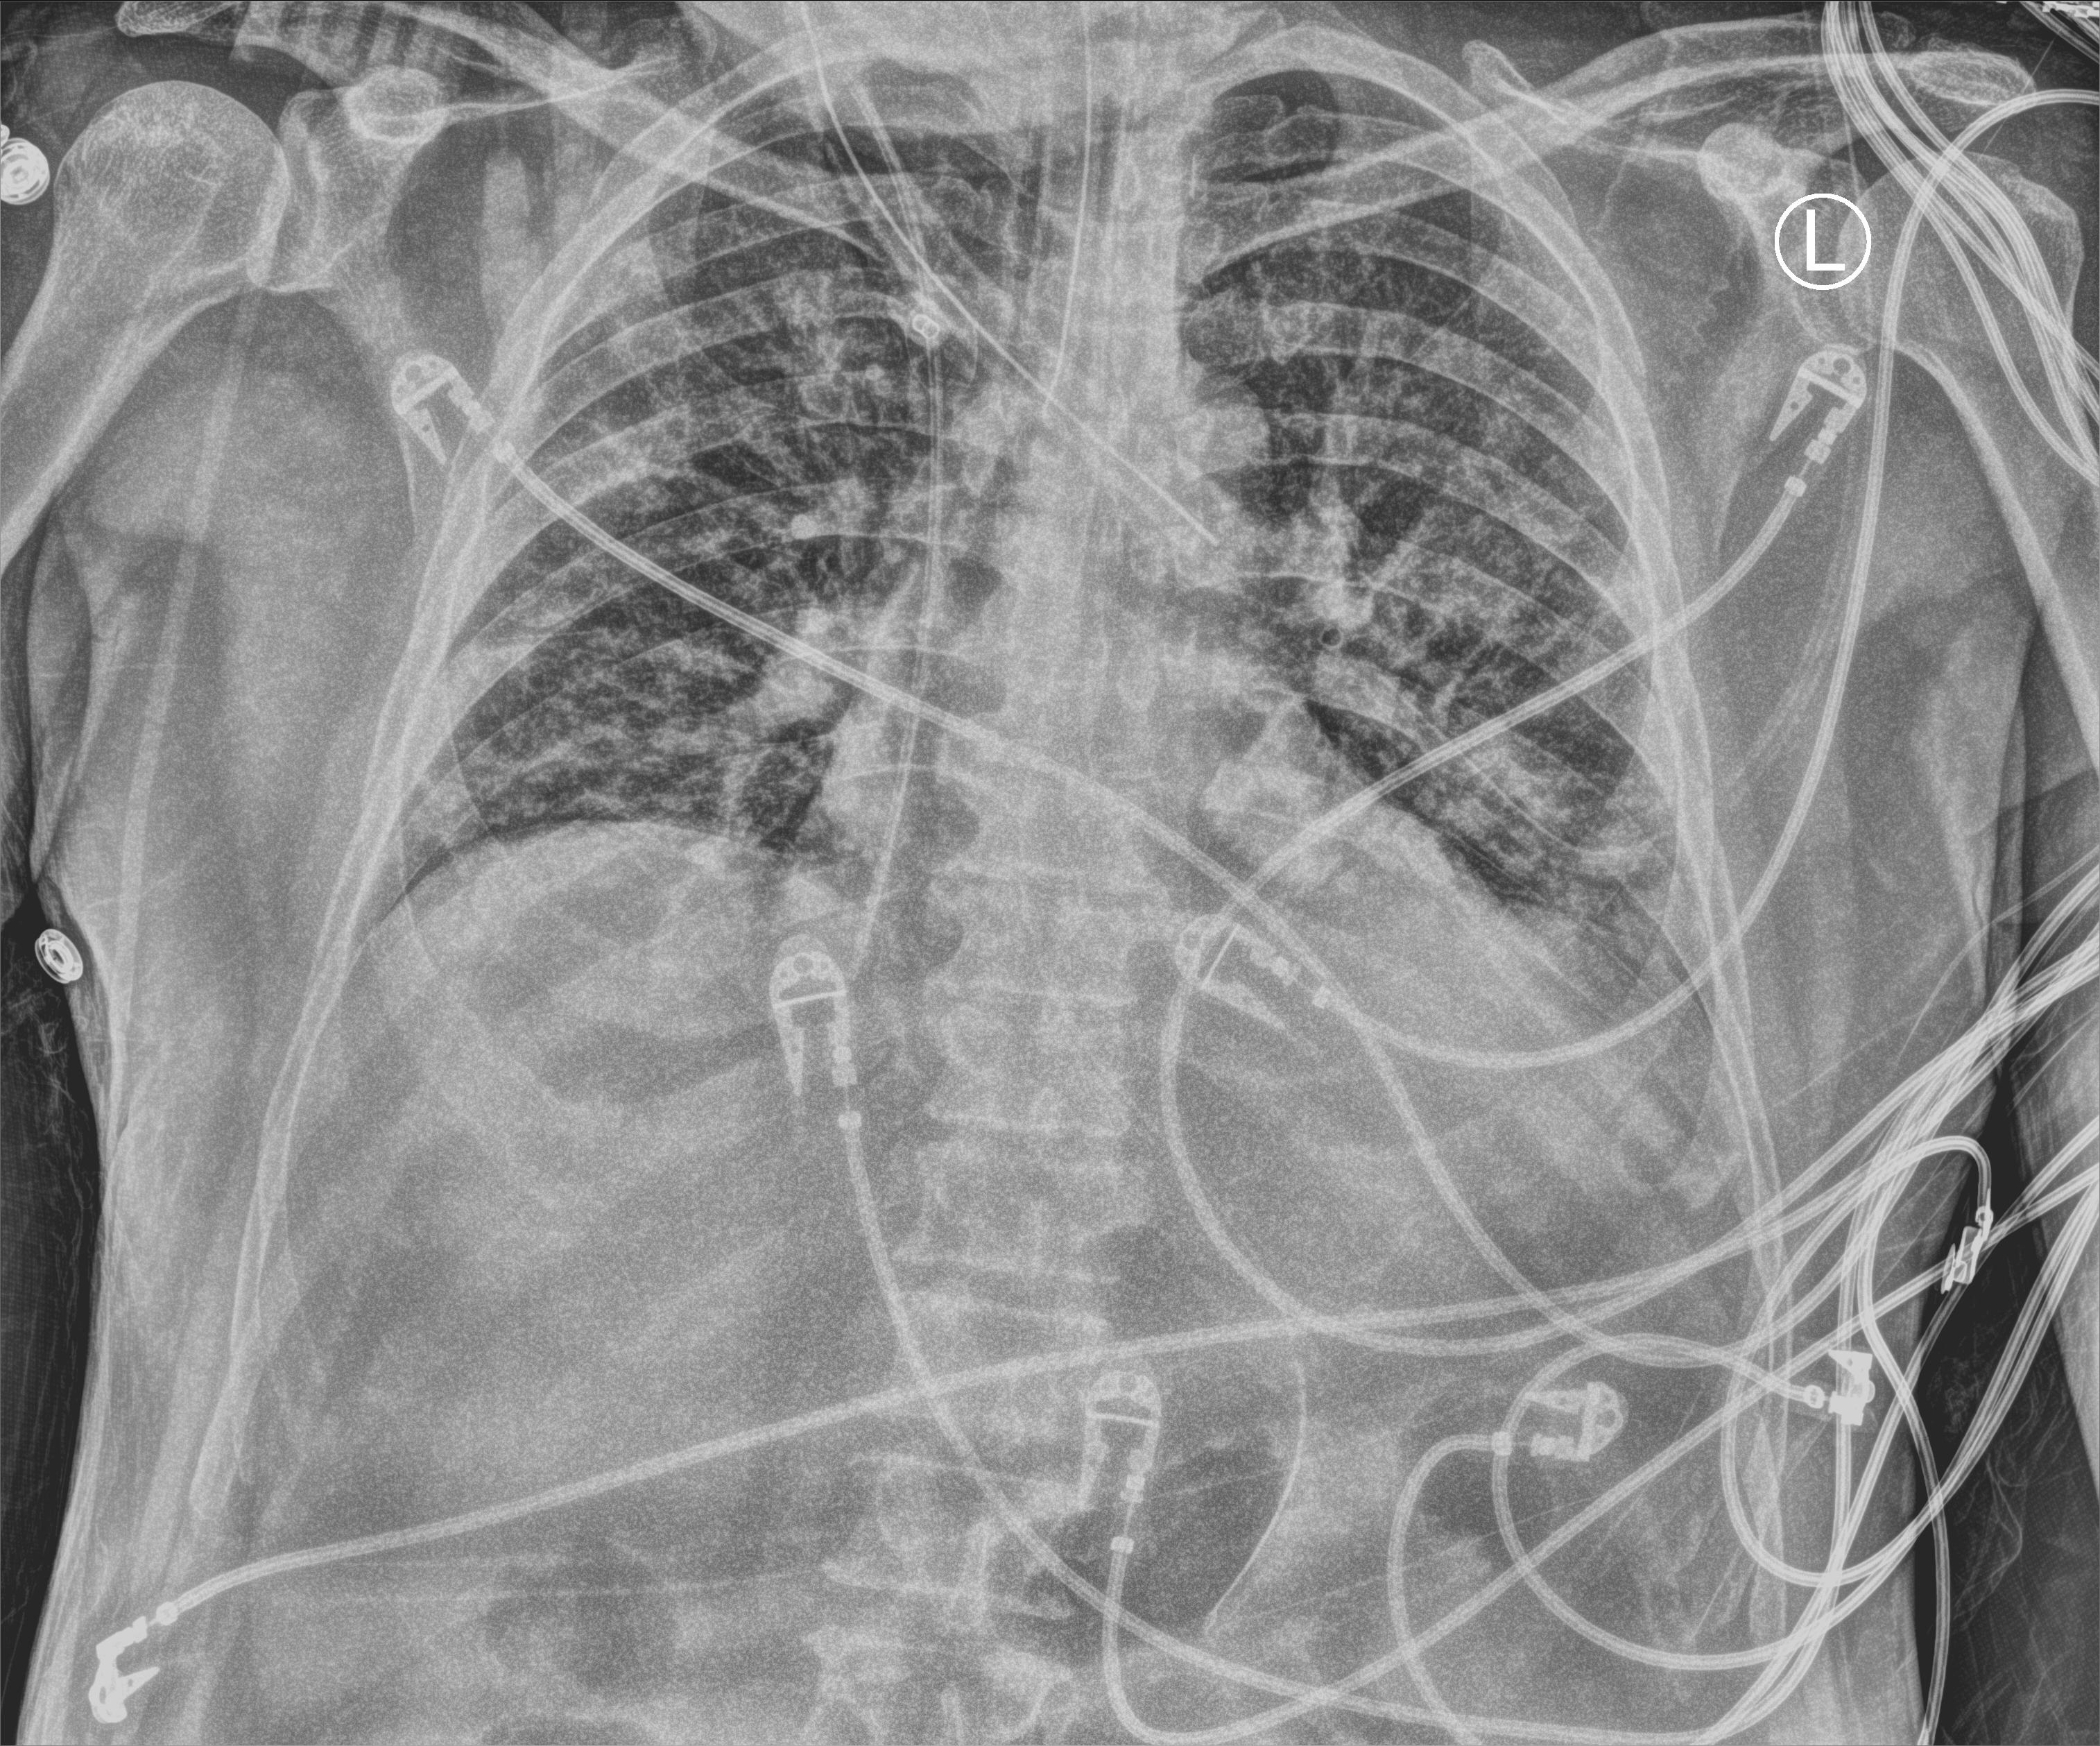
Chest X-ray (portable), anteroposterior (AP) projection. Patient hospitalised with COVID-19; male, aged 18–59 years.
Admission-level facts for this patient (not findings on this image; timing relative to this image not recorded): chronic kidney disease (admission record): no; admitted to intensive care during this hospital stay: yes.